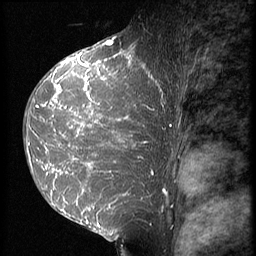
Breast MRI (dynamic contrast-enhanced), one sagittal slice. Position 37 of 64 along the scan axis. 3 images stored at this slice position (order not interpretable as contrast timing). 1.5 T. TE 4.2 ms, TR 9 ms. 2.5 mm slice thickness. 256 × 256 image matrix, field of view 180 × 180 mm. Female patient, age 39 years. From the clinical record (not read from this slice): setting: breast cancer imaged before/during neoadjuvant chemotherapy; receptor status: HER2-positive.
Outlined on this slice (semi-automatic segmentation, software-assisted and operator-edited):
- analysis volume of interest (the breast-tissue region the enhancement analysis was run in; not a lesion): box from (x=23, y=47) to (x=161, y=239) px
- tumour enhancement mask (voxels above the 140 % enhancement threshold inside the analysis volume of interest): (x=26, y=48)–(x=158, y=227)